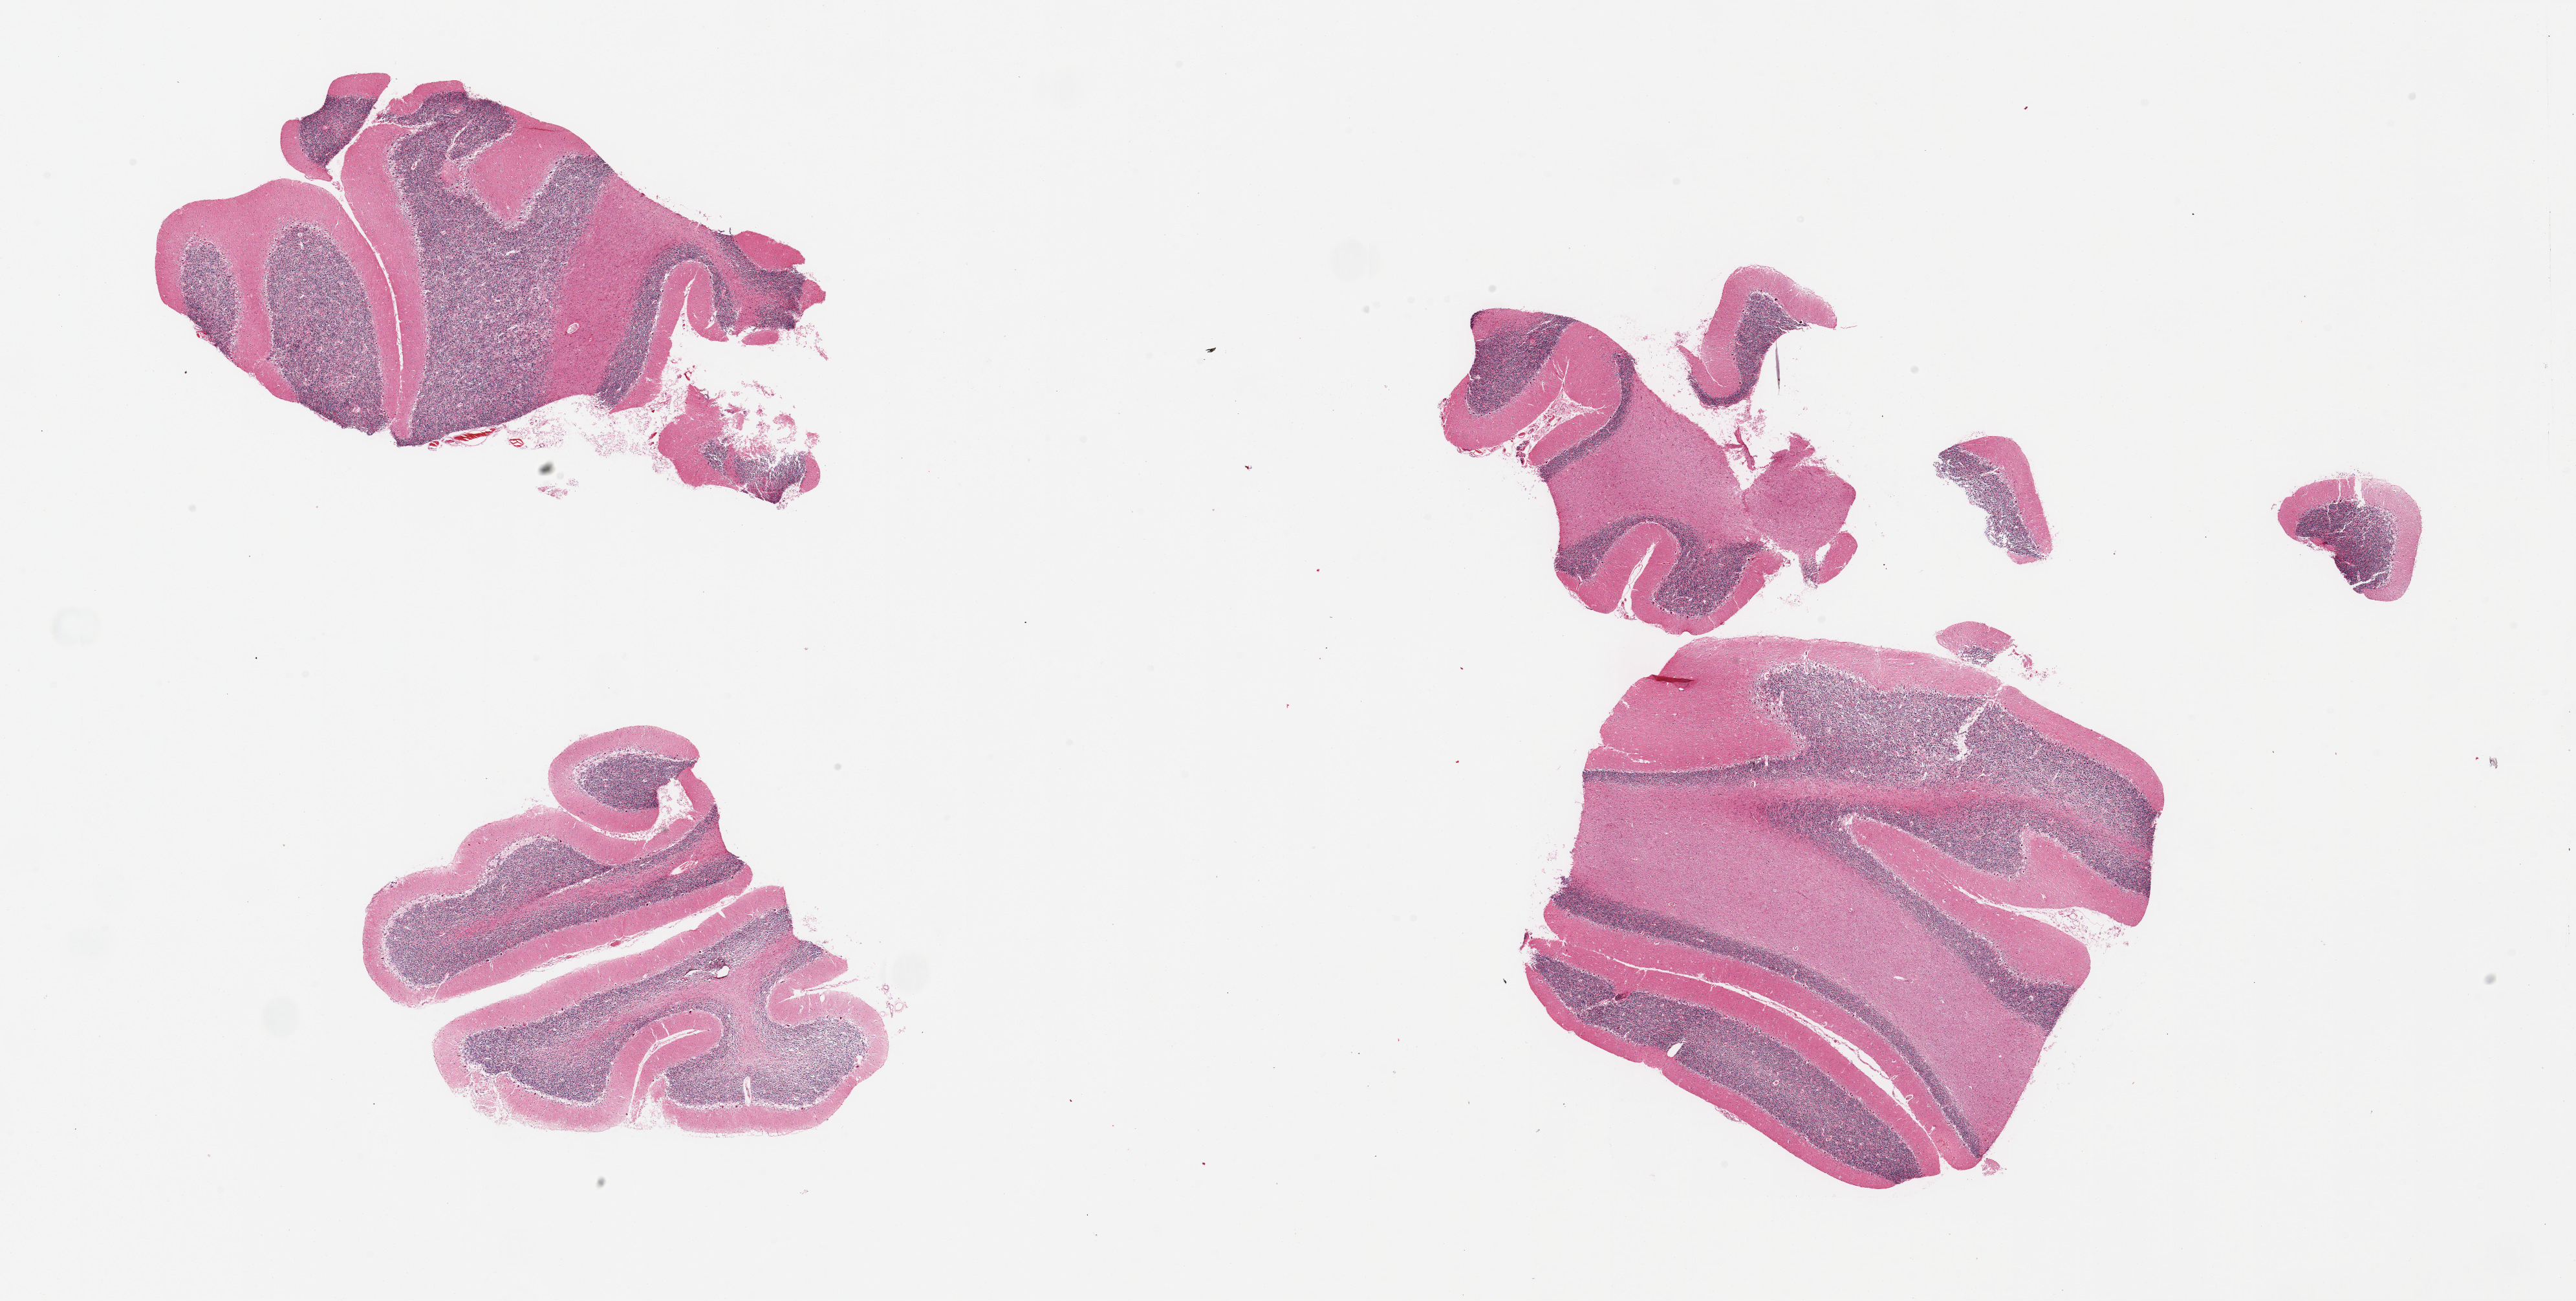
Haematoxylin and eosin whole-slide image — whole scanned area (about 31.5 x 15.9 mm) shown as a low-resolution overview; PAXgene-fixed, paraffin-embedded tissue; section of cerebellum (target tissue); donor tissue sample. Donor: male.
Reviewer comment on this tissue sample: 4 fragmented pieces; Purkinje cells present.